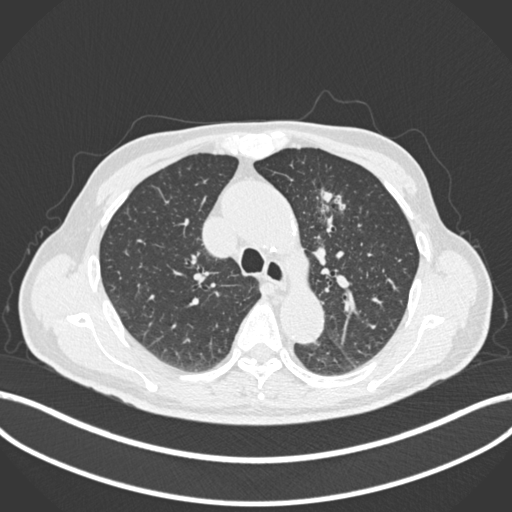
Chest CT, one axial slice; position 174 of 261 along the scan axis; 120 kVp; lung window (W 1500 / L -600 HU); 1 mm slice thickness; 512 × 512 image matrix, field of view 400 × 400 mm. Patient: male, 74 years. Case-level facts recorded for this patient, not image findings: clinical TNM (as recorded): T2b N0 M1c.
Structures marked on this image (rectangle marked by the reading radiologist):
- lung tumour (recorded histology: adenocarcinoma): bounding box [x1, y1, x2, y2] px = [312, 185, 355, 222]